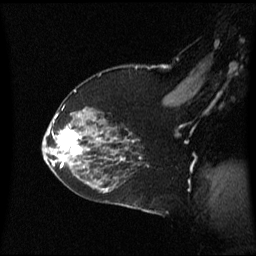
Breast MRI (dynamic contrast-enhanced), one sagittal slice; position 44 of 60 along the scan axis; dynamic contrast-enhanced series, image 2 of 3 at this slice position (ordered by acquisition); 1.5 T; TE 4.2 ms, TR 8.4 ms; 2 mm slice thickness; 256 × 256 image matrix, field of view 240 × 240 mm. Patient: female, 59 years. From the clinical record (not read from this slice): setting: breast cancer imaged before/during neoadjuvant chemotherapy; receptor status: HR-positive, HER2-negative.
Structures marked on this image (semi-automatically segmented with operator editing):
- analysis volume of interest (the breast-tissue region the enhancement analysis was run in; not a lesion): box from (x=46, y=114) to (x=89, y=163) px
- tumour enhancement mask (voxels above the 70 % enhancement threshold inside the analysis volume of interest): (x=58, y=128)–(x=81, y=155)